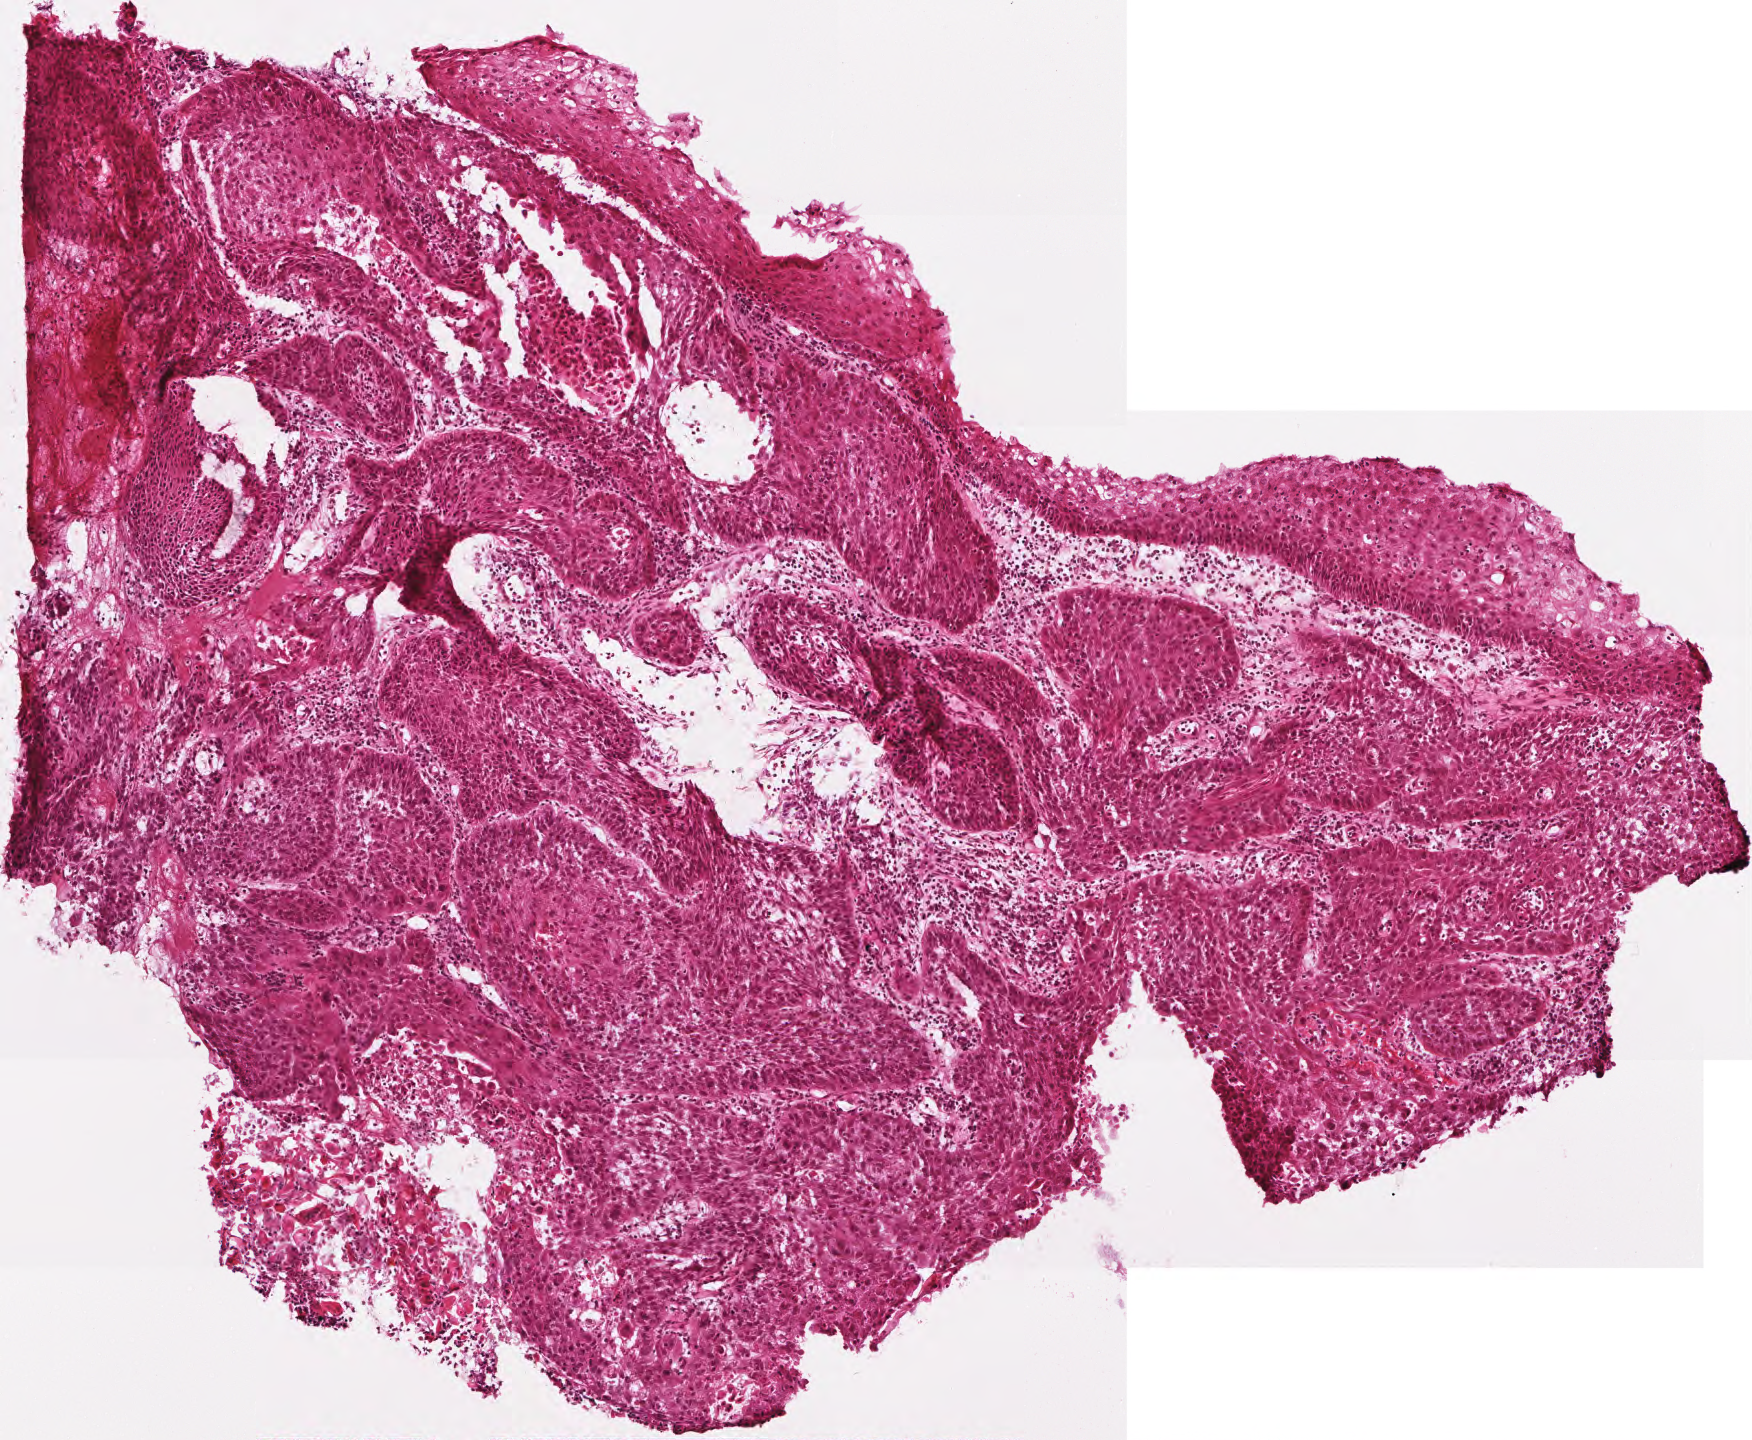
Whole-slide histology image, Hematoxylin and eosin (H&E) stained — a low-resolution overview of the entire scanned area, about 3.5 x 2.9 mm, frozen section, sample: primary tumour, head and neck. Female patient; age at initial diagnosis 45 years. Slide review estimates, as recorded: tumour cells 90%, tumour nuclei 65%.
Histologic diagnosis: Squamous cell carcinoma, NOS (larynx, NOS).